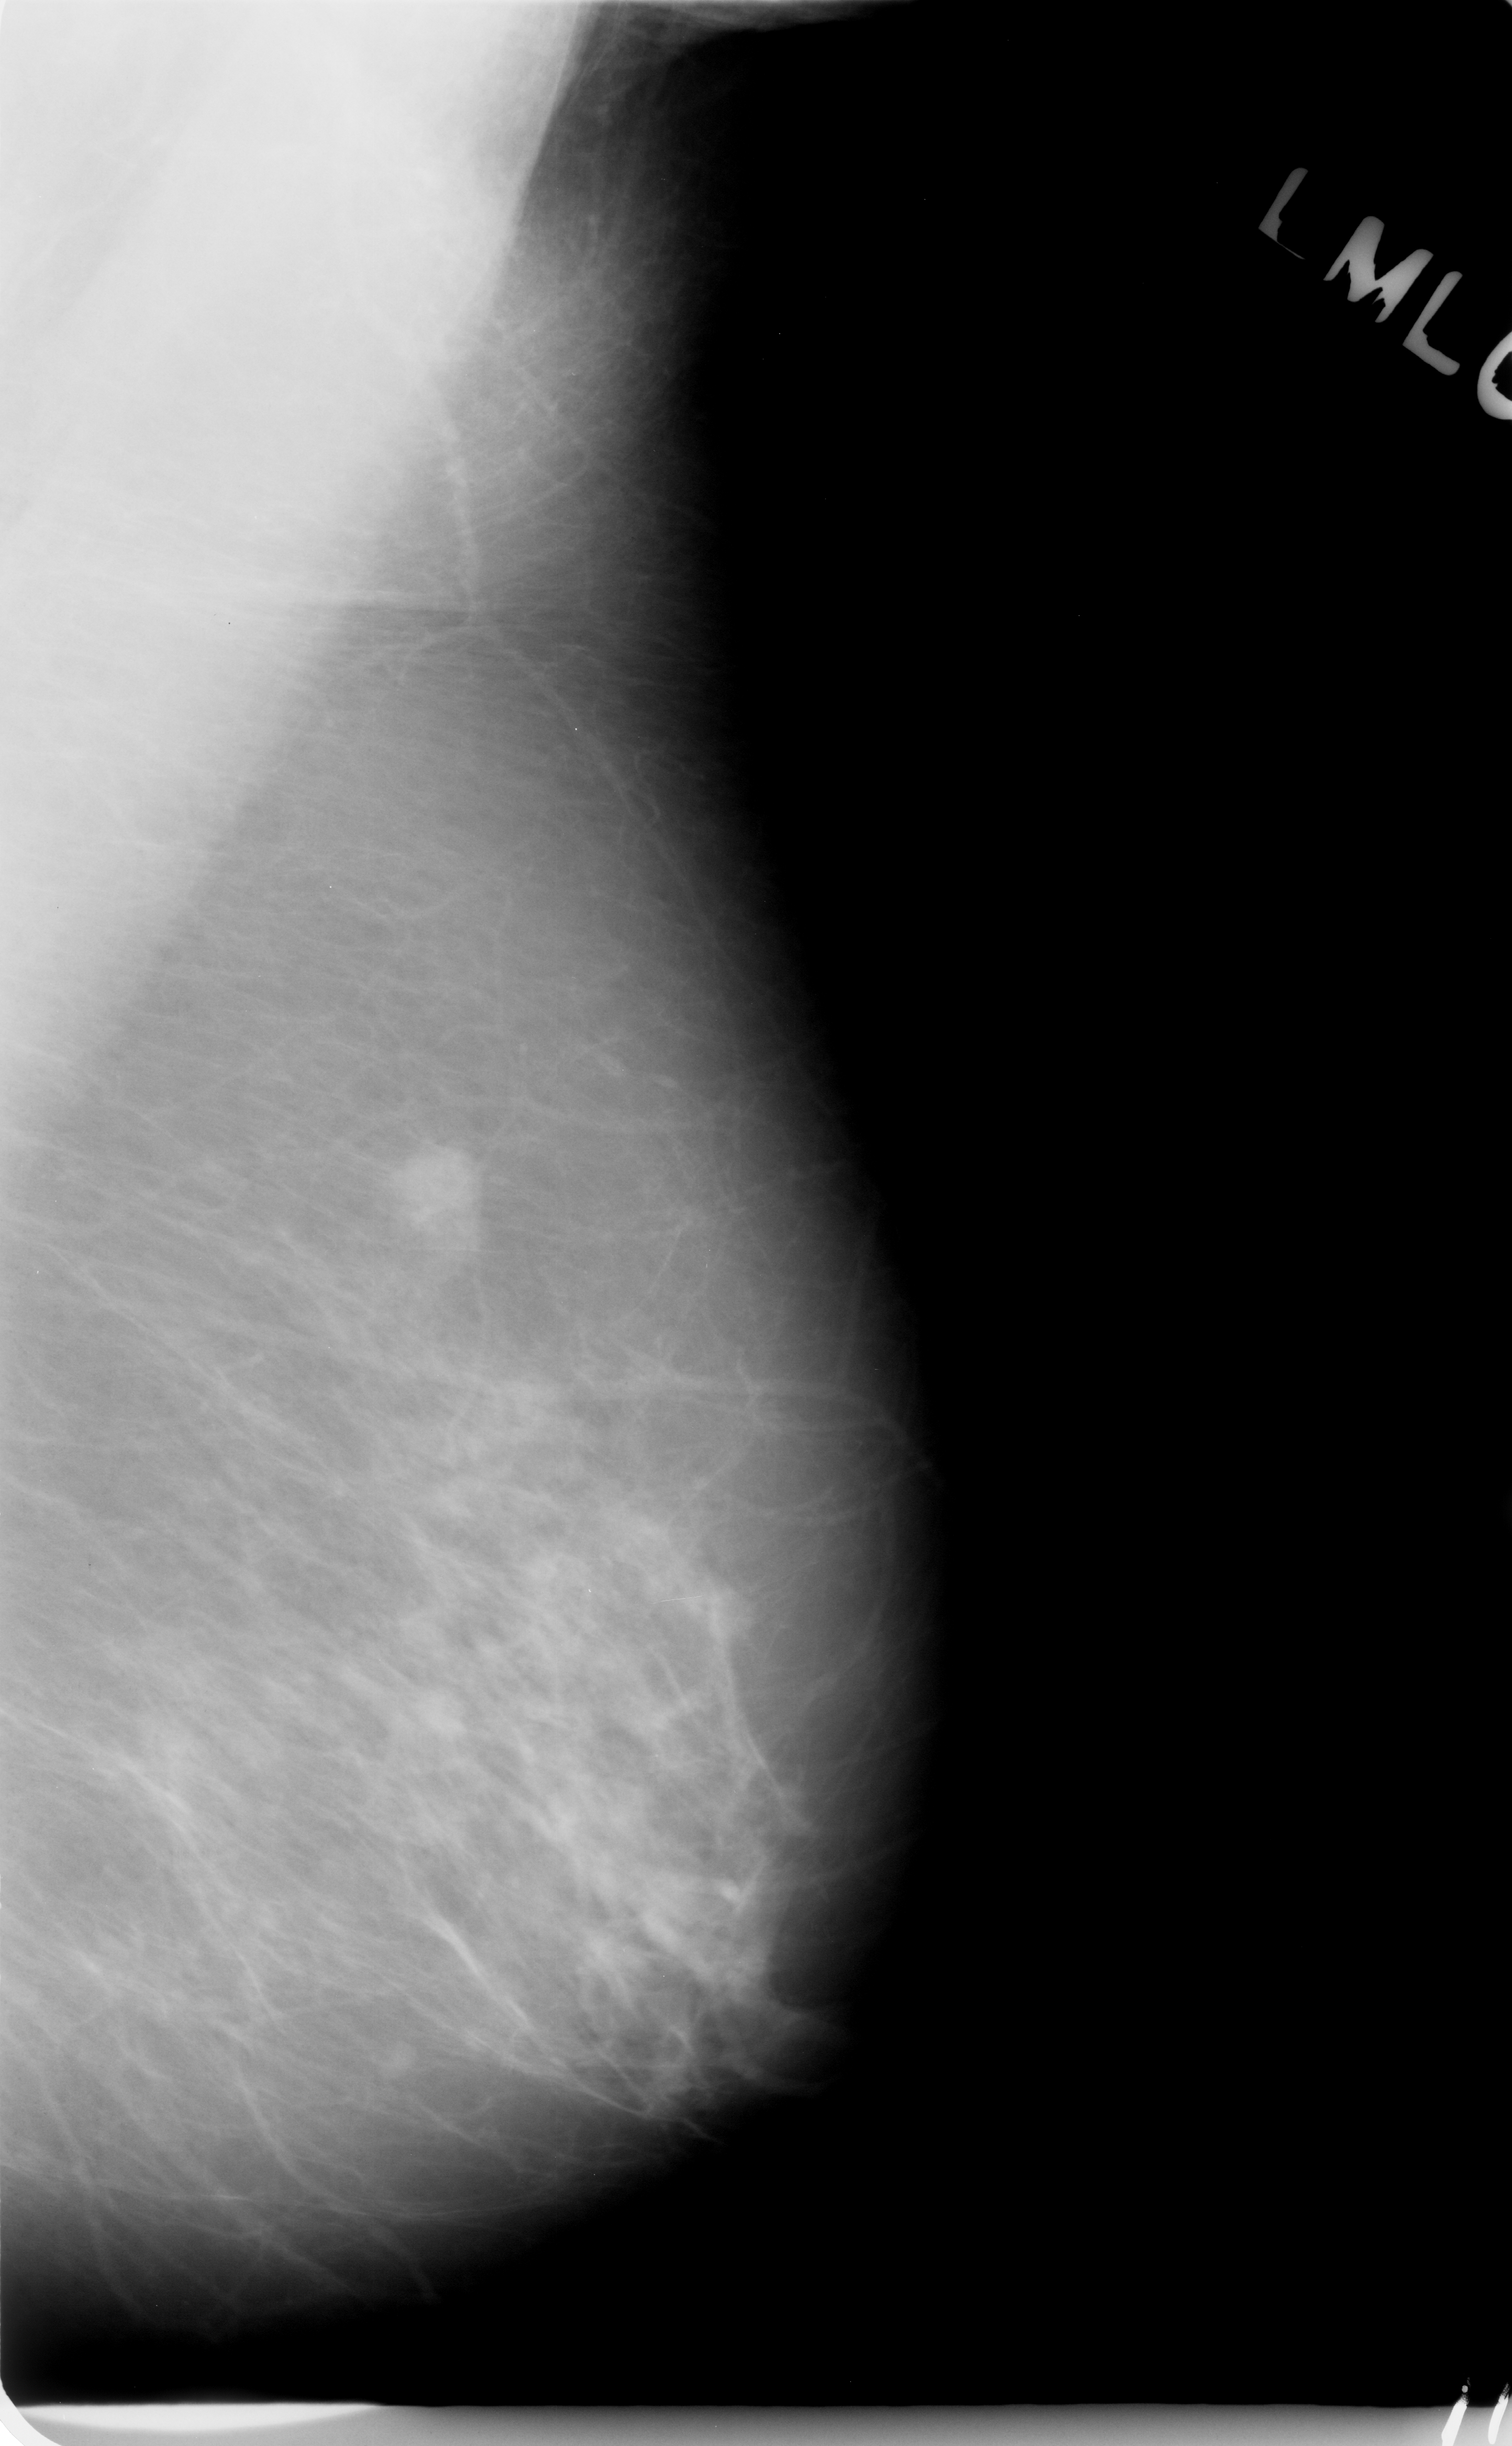
Scanned film-screen mammogram, left breast, mediolateral oblique (MLO) view, breast composition: scattered fibroglandular densities (BI-RADS density category 2 of 4).
- Finding: mass, shape lobulated, margins spiculated; BI-RADS assessment category 5; pathology (as recorded): malignant.